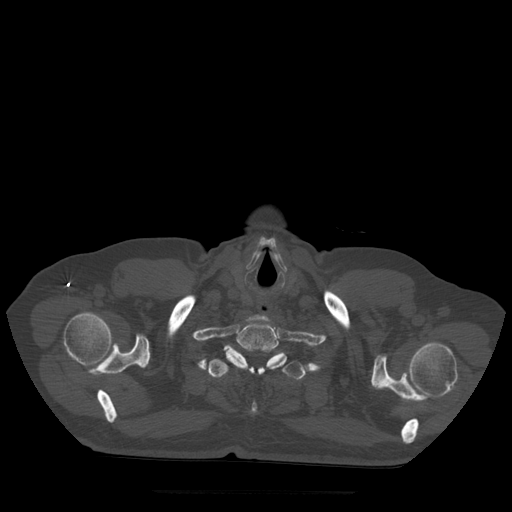
CT including the spine, one axial slice; slice 435 of 522 in the series (ordered by position); bone window (W 1800 / L 400 HU); 1.25 mm slice thickness; 512 × 512 image matrix, field of view 420 × 420 mm. Patient age 72 years. From the clinical record (not read from this slice): primary cancer: prostate.
Outlined on this slice (semi-automatic segmentation, software-assisted and operator-edited):
- T1 vertebra: bounding box [x1, y1, x2, y2] px = [224, 320, 287, 369]
- T2 vertebra: [208, 345, 306, 414]